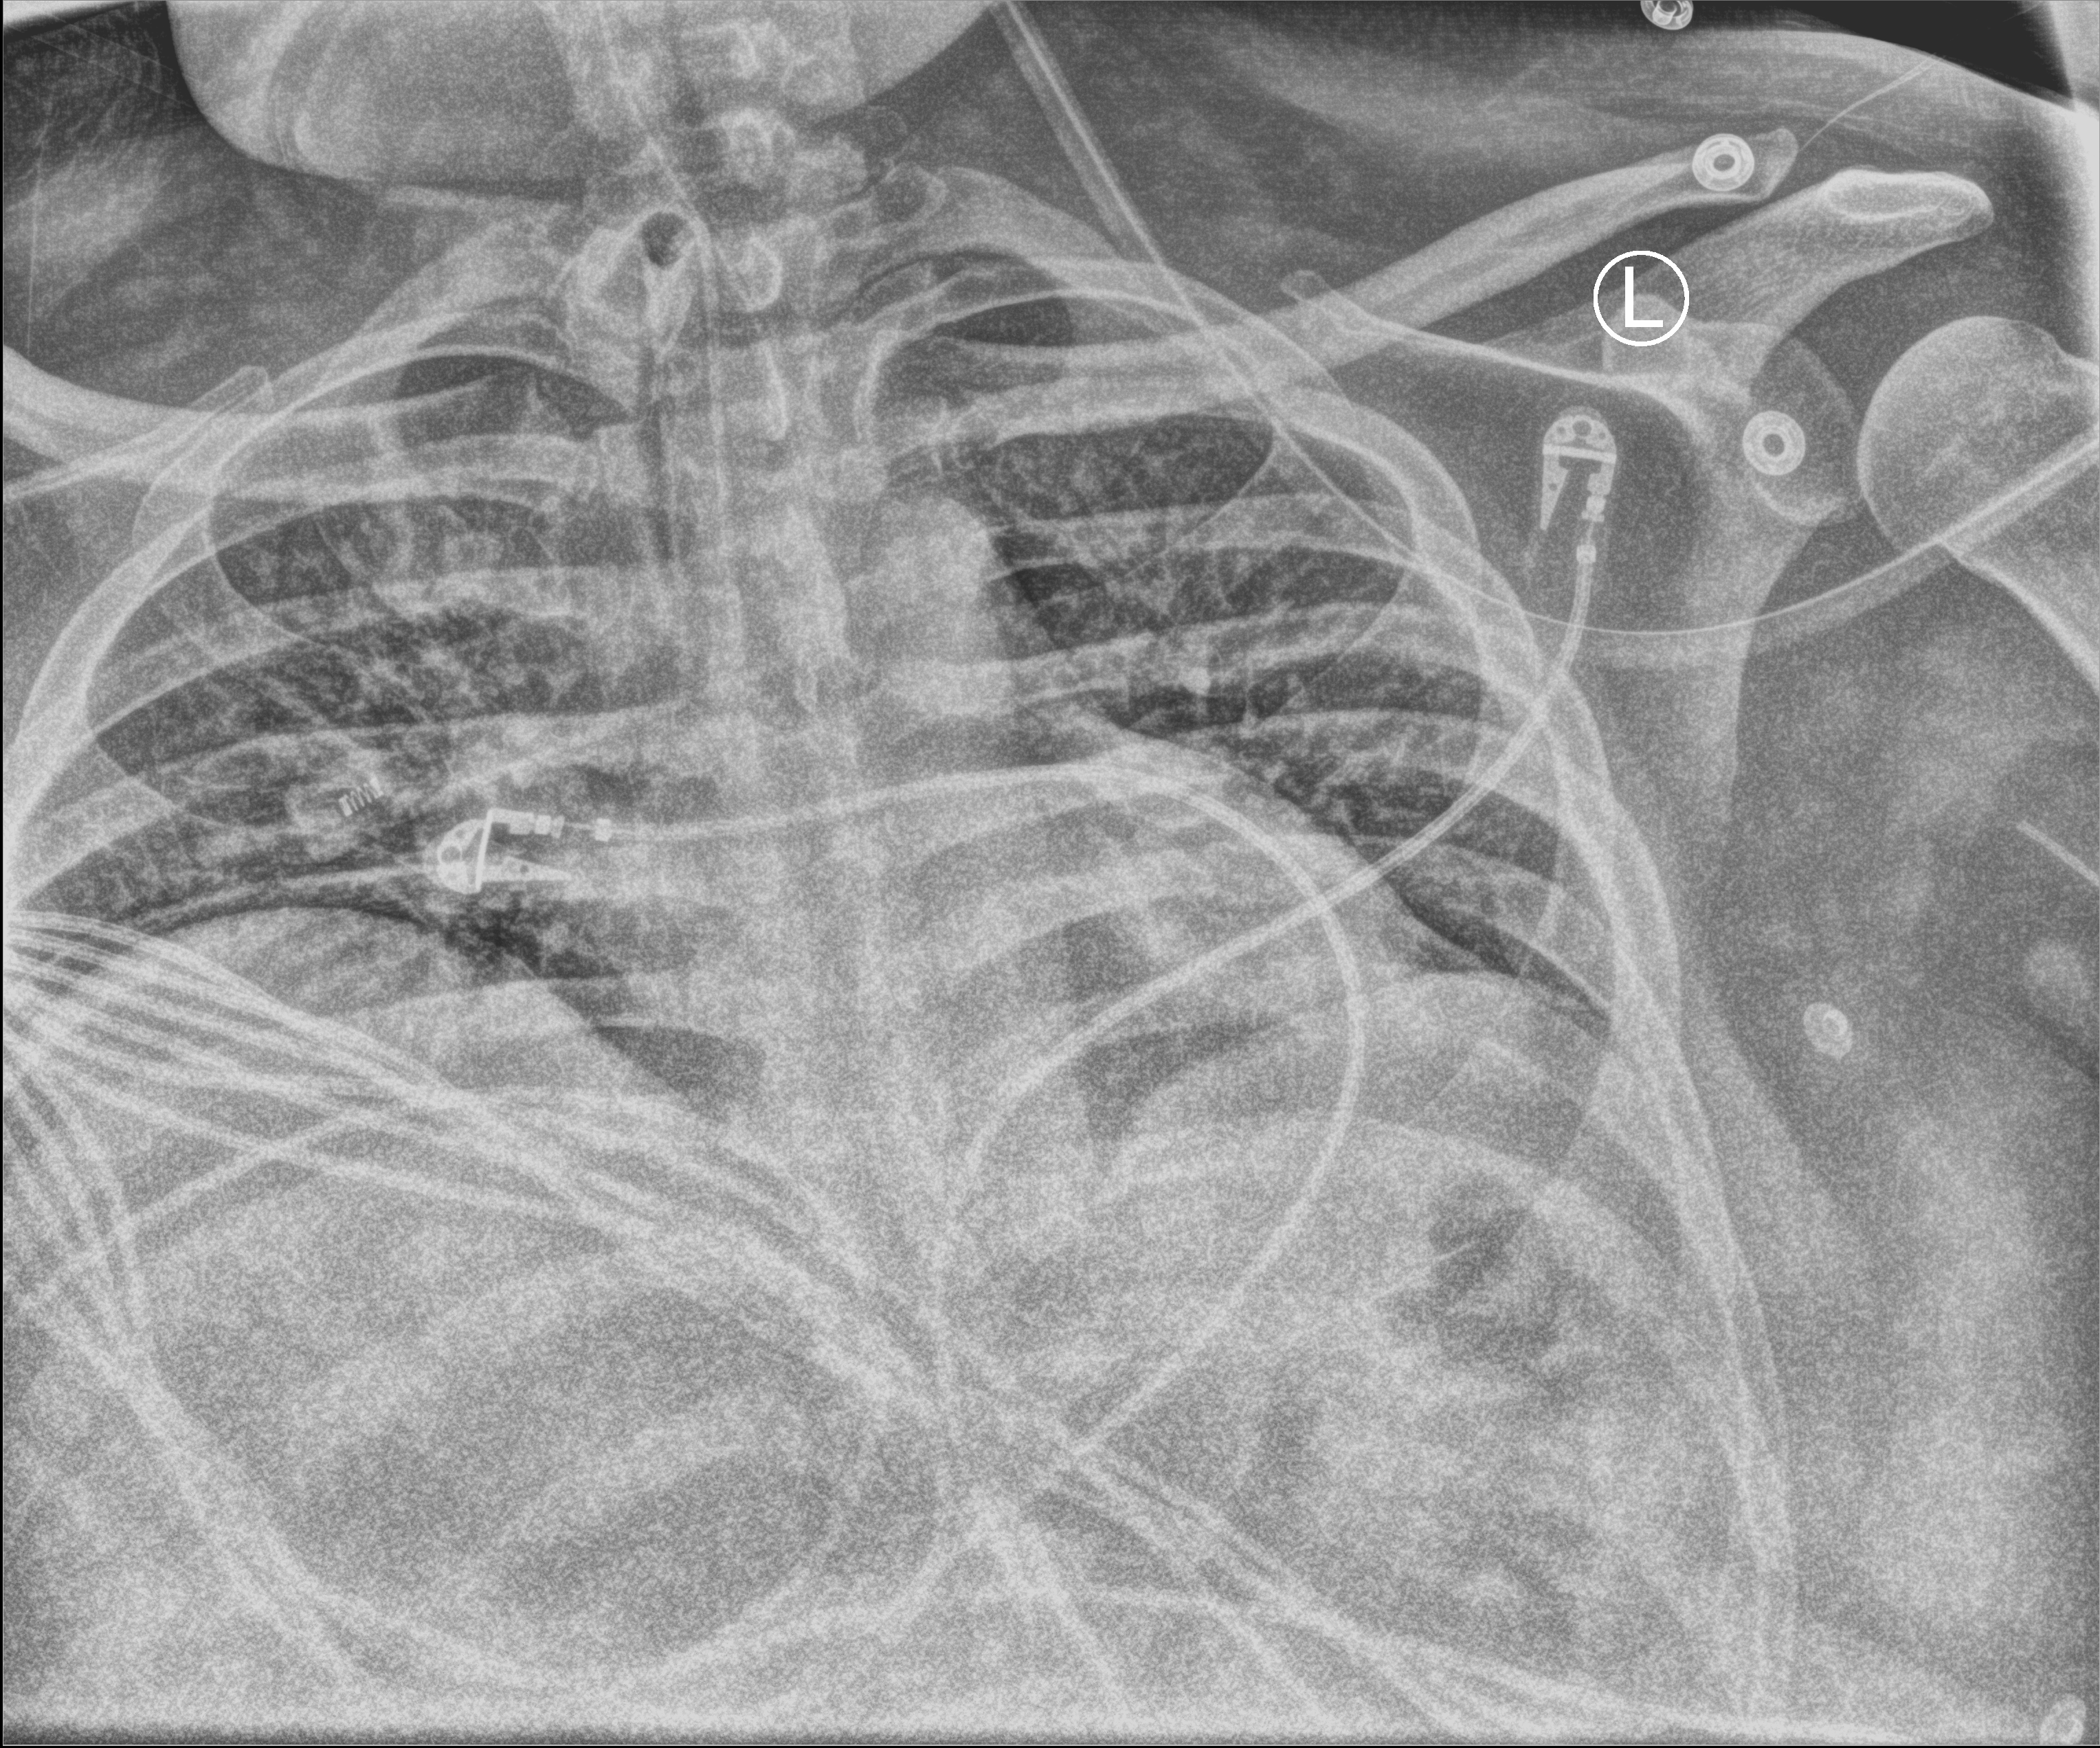
Portable chest radiograph. Male patient hospitalised with COVID-19, age 18–59 years.
From the hospital-stay record, not from the radiograph (when in the stay this image was taken is not recorded):
- mechanically ventilated during this hospital stay: yes
- admitted to intensive care during this hospital stay: yes
- length of hospital stay: 69 days